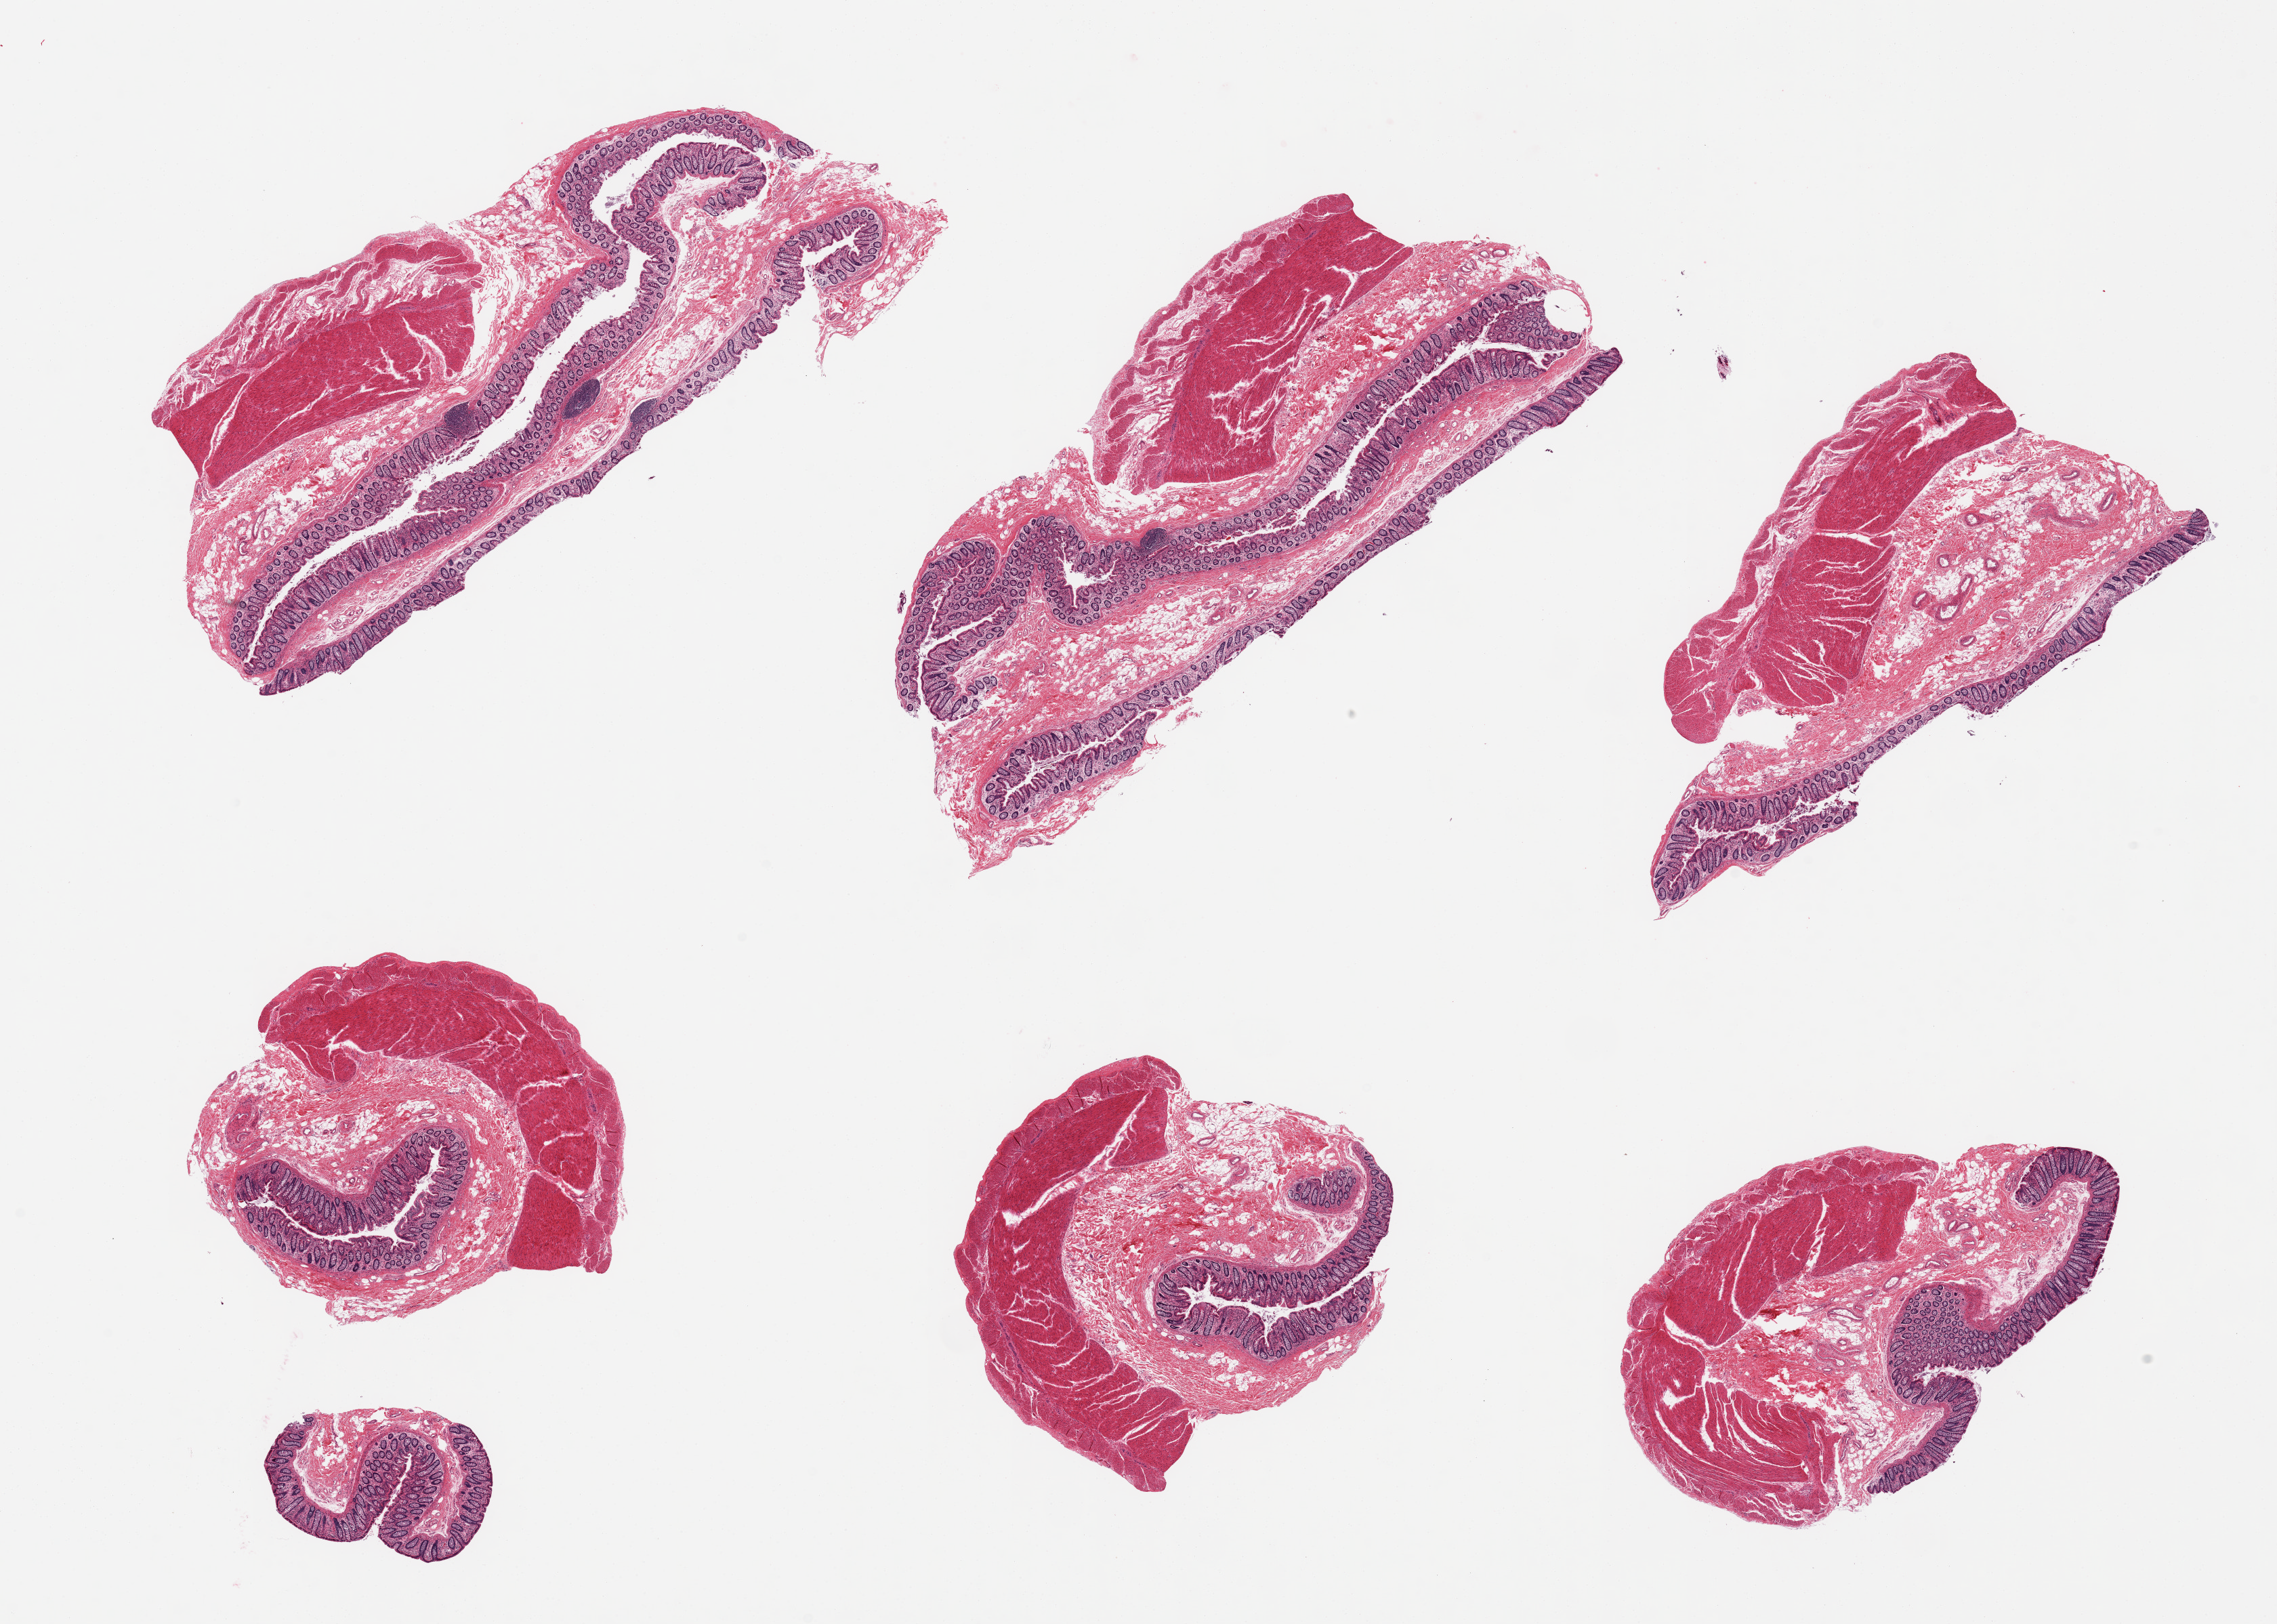
Whole-slide image, haematoxylin and eosin stain, brightfield — whole scanned area (about 26.6 x 19.0 mm, acquisition: 20x scan) shown as a low-resolution overview. PAXgene-fixed, paraffin-embedded tissue. Sampled site (target tissue): transverse colon. Donor tissue sample.
Pathologist's review note for this sample: 6 pieces, mucosa well preserved, ~0.35mm, ~10% thickness.